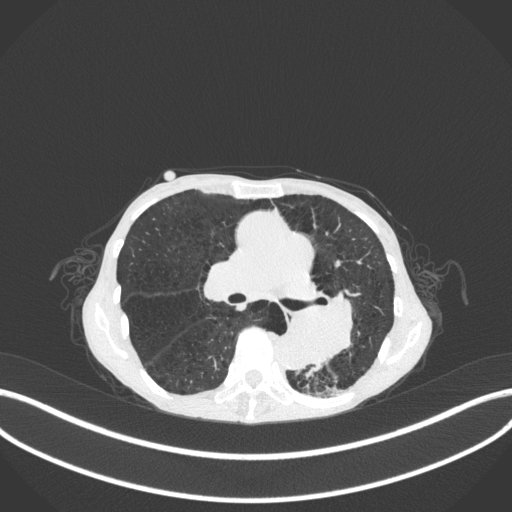
Chest CT, one axial slice; position 159 of 347 along the scan axis; reconstruction kernel B31f; 120 kVp; lung window (W 1500 / L -600 HU); 1 mm slice thickness; 512 × 512 image matrix. Female patient, age 70 years. From the clinical record (not read from this slice): clinical TNM (as recorded): T3 N0 M0.
Outlined on this slice (rectangle marked by the reading radiologist):
- lung tumour (recorded histology: small cell carcinoma): bounding box (x1, y1, x2, y2) in pixels: (280, 282, 362, 371)